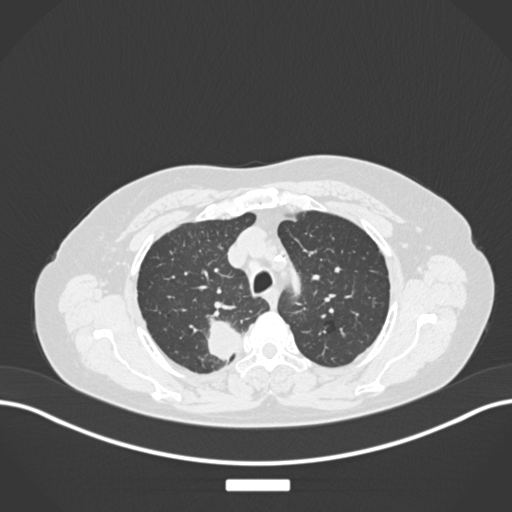
Chest CT, one axial slice. Position 202 of 237 along the scan axis. 120 kVp. Lung window (W 1500 / L -600 HU). 1 mm slice thickness. 512 × 512 image matrix. Female patient, age 62 years. From the clinical record (not read from this slice): clinical TNM (as recorded): T1c N1 M0.
Structures marked on this image (rectangle marked by the reading radiologist):
- lung tumour (recorded histology: squamous cell carcinoma): bounding box <203,317,246,362> (left, top, right, bottom; pixels)